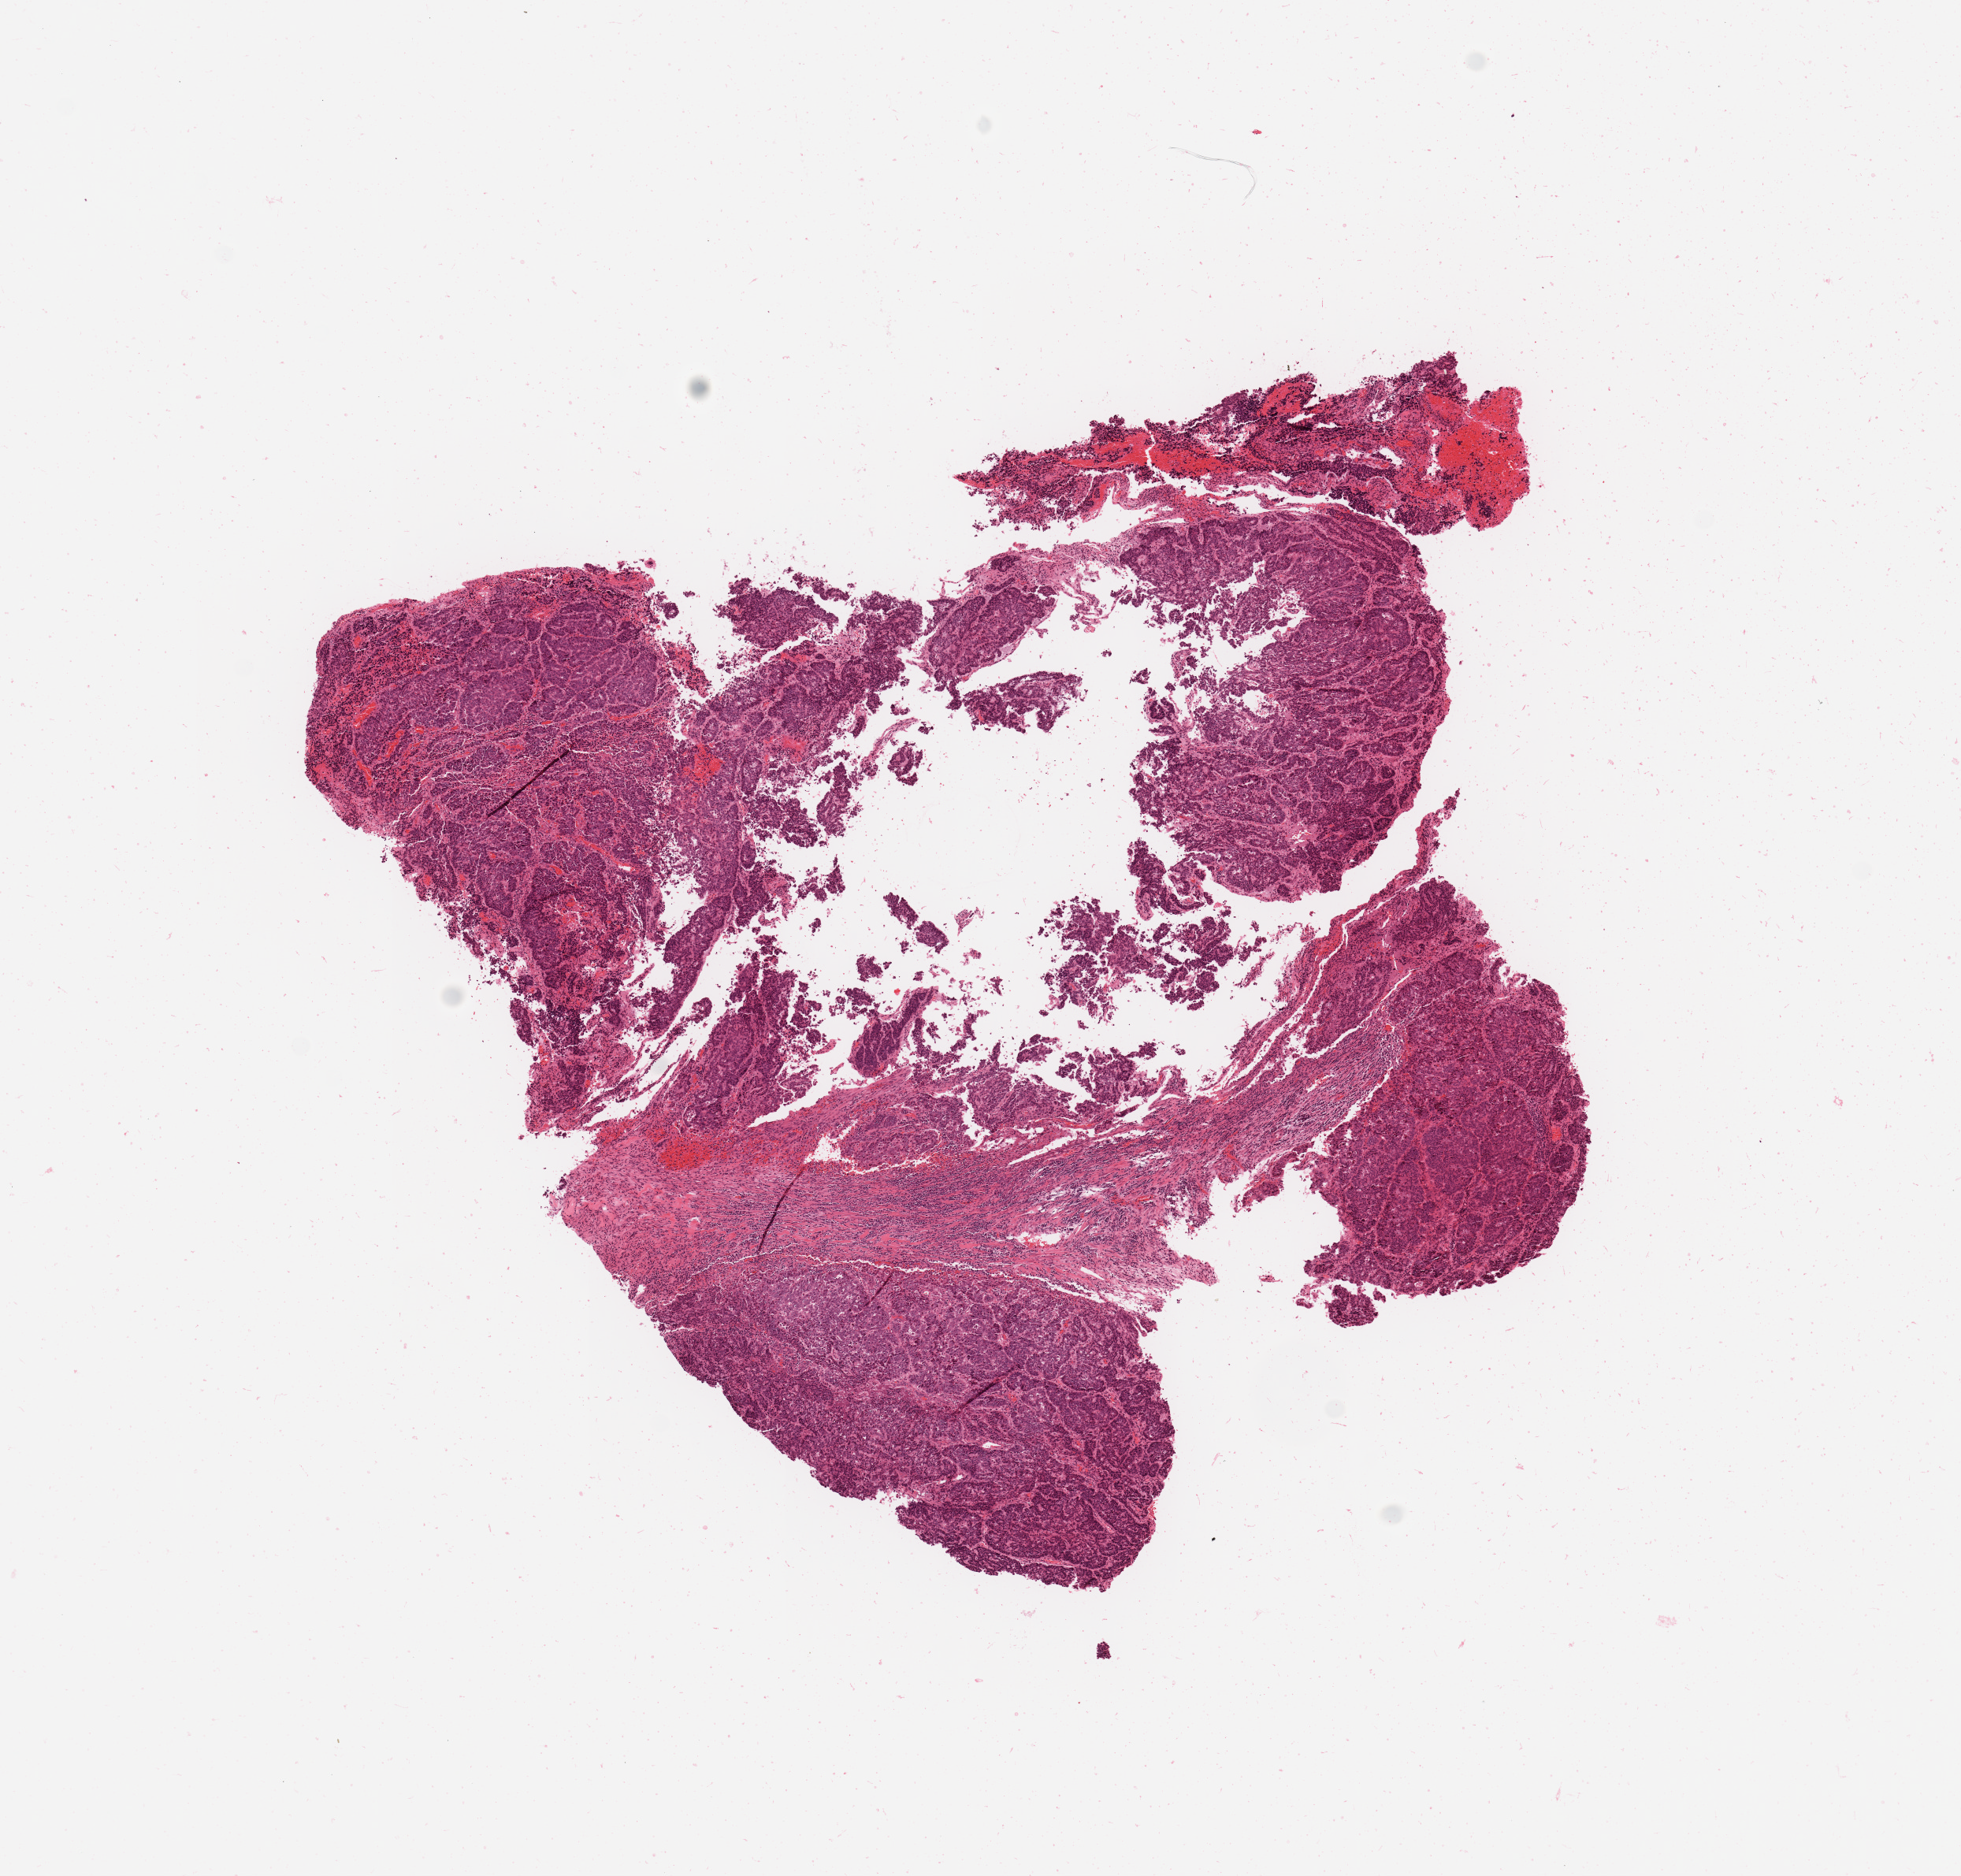
Digitized H&E tissue section (whole slide) — low-resolution overview of the scanned area, about 9.8 x 9.4 mm (from a 20x scan); tumour tissue sample, uterus. Female, 73 y/o. Histologic grade: G3 (poorly differentiated).
Histologic diagnosis: Endometrioid adenocarcinoma, NOS. AJCC pathologic stage: IA.